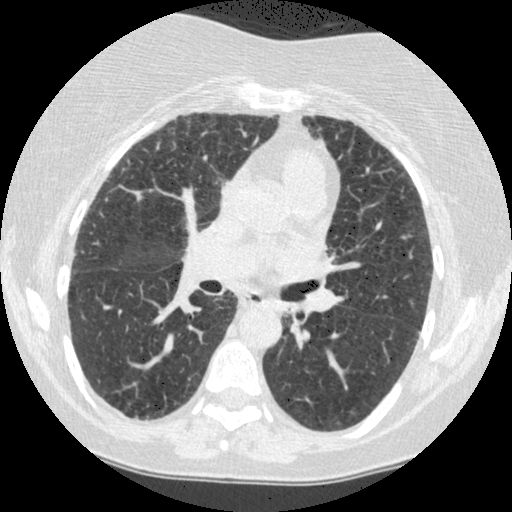
Axial slice from a low-dose chest CT screening exam; baseline screening round; lung window (W 1500 / L -600 HU); 1.25 mm slice thickness; 120 kVp. Female participant, aged 60 years at enrolment. Former smoker at enrolment.
Expert reader's lesion annotation, bounding box [x1, y1, x2, y2] px = [271, 294, 311, 336]. The screening reader recorded 2 non-calcified nodules or masses ≥4 mm on this exam (right lower lobe, left lower lobe); which of them this box marks is not recorded. Official screen result: positive, change unspecified: nodule(s) >= 4 mm or enlarging nodule(s), mass(es), or other non-specific abnormalities suspicious for lung cancer. Later outcome: lung cancer diagnosed 794 days after this screen (after the third annual screen) — small cell carcinoma, NOS, left lower lobe, undifferentiated (G4), stage IV (AJCC 6th edition), 69 mm at pathology.